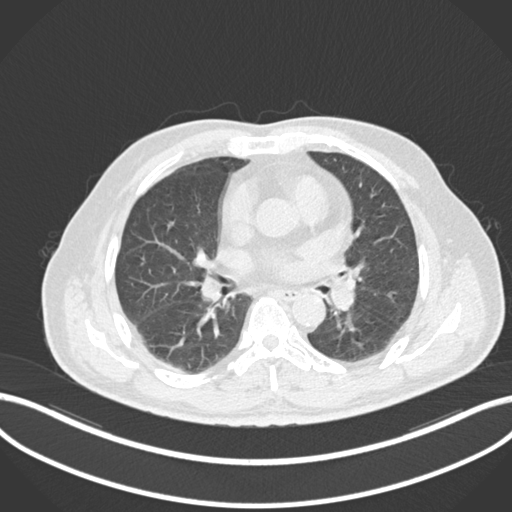
Chest CT, one axial slice. Position 71 of 161 along the scan axis. 120 kVp. Lung window (W 1500 / L -600 HU). 1 mm slice thickness. 512 × 512 image matrix. Male patient, age 71 years. Case-level facts recorded for this patient, not image findings: clinical TNM (as recorded): T1b N0 M0.
Annotated regions visible in this slice (rectangle marked by the reading radiologist):
- lung tumour (recorded histology: squamous cell carcinoma): bounding box [x1, y1, x2, y2] px = [327, 276, 357, 314]